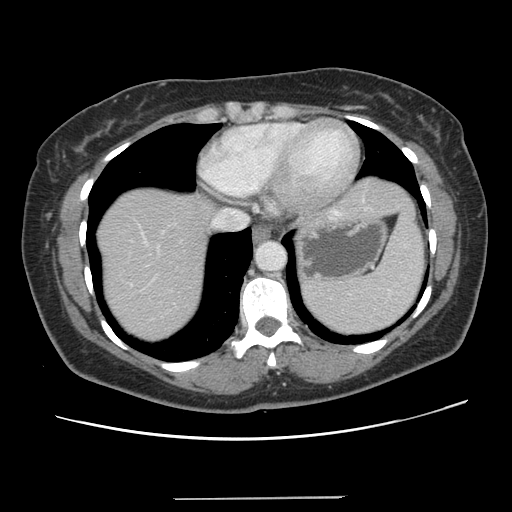
Contrast-enhanced abdominal CT, one axial slice; slice 119 of 141 in the series (ordered by position); 120 kVp; soft-tissue window (W 400 / L 40 HU); 2.5 mm slice thickness; 512 × 512 image matrix. Female patient, age 53 years. Case-level facts recorded for this patient, not image findings: diagnosis: colorectal cancer liver metastases, imaged before liver resection; multiple liver metastases: no; largest metastasis: 14.5 cm; disease in both lobes: yes.
Structures marked on this image (outlined manually by an expert reader):
- hepatic veins: box from (x=137, y=209) to (x=245, y=278) px
- liver: (x=96, y=178)–(x=410, y=343)
- planned liver remnant (the part of the liver to remain after resection): (x=96, y=214)–(x=210, y=342)